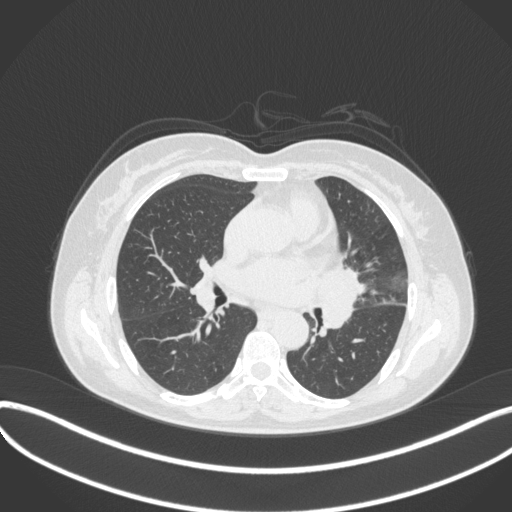
Chest CT, one axial slice; slice 184 of 373 in the series (ordered by position); 120 kVp; lung window (W 1500 / L -600 HU); 512 × 512 image matrix, field of view 400 × 400 mm. Patient: female, 54 years. From the clinical record (not read from this slice): clinical TNM (as recorded): T2a N1 M0.
Structures marked on this image (bounding box drawn by a radiologist):
- lung tumour (recorded histology: small cell carcinoma): bounding box [x1, y1, x2, y2] px = [315, 268, 369, 338]